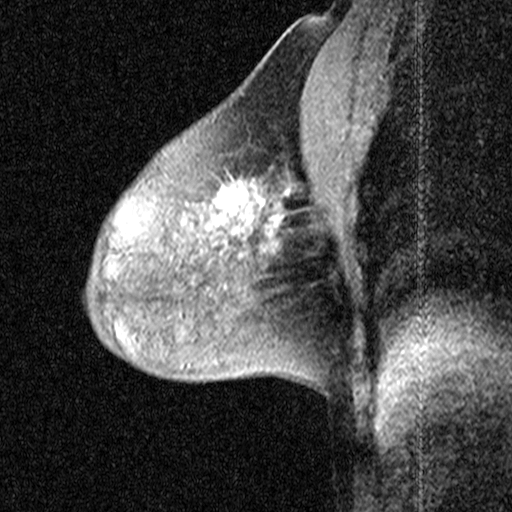
Breast MRI (dynamic contrast-enhanced), one sagittal slice; slice 28 of 44 in the series (ordered by position); dynamic contrast-enhanced study with each time point stored as its own series, time point 2 of 3 at this slice position (early post-contrast, ordered by acquisition time); 1.5 T; TE 4.5 ms, TR 11 ms; 3 mm slice thickness; 512 × 512 image matrix, field of view 200 × 200 mm. Patient: female, 53 years. Case-level facts recorded for this patient, not image findings: setting: breast cancer imaged before/during neoadjuvant chemotherapy; receptor status: HR-positive, HER2-negative.
Outlined on this slice (semi-automatic segmentation, software-assisted and operator-edited):
- analysis volume of interest (the breast-tissue region the enhancement analysis was run in; not a lesion): bounding box [x1, y1, x2, y2] px = [198, 152, 299, 267]
- tumour enhancement mask (voxels above the 90 % enhancement threshold inside the analysis volume of interest): [200, 188, 288, 231]